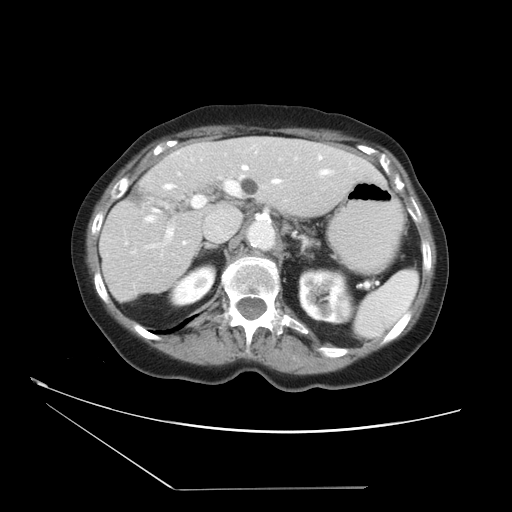
Contrast-enhanced abdominal CT, one axial slice. Position 22 of 36 along the scan axis. Intravenous contrast given. Soft-tissue window (W 400 / L 40 HU). 5 mm slice thickness. 512 × 512 image matrix. Female patient, age 81 years. From the clinical record (not read from this slice): diagnosis: colorectal cancer liver metastases, imaged before liver resection; multiple liver metastases: no; largest metastasis: 1.6 cm; chemotherapy before resection: no.
Annotated regions visible in this slice (outlined manually by an expert reader):
- hepatic veins: bounding box <131,157,334,284> (left, top, right, bottom; pixels)
- liver: <100,137,385,302>
- planned liver remnant (the part of the liver to remain after resection): <100,139,384,302>
- portal vein (with intrahepatic branches): <132,177,243,254>
- liver metastasis: <241,177,259,197>